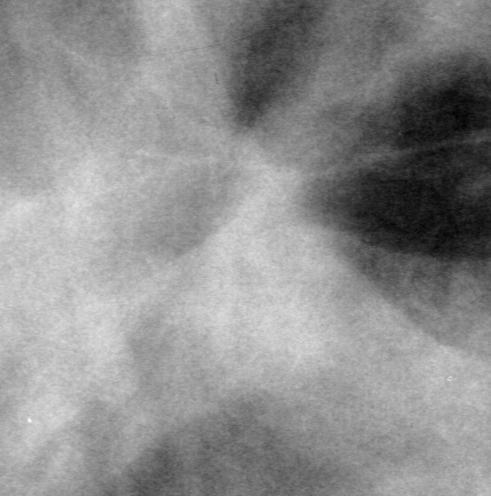
Region of interest cut from a scanned film mammogram (one marked finding), right breast, CC view, BI-RADS breast density category 4 (scale 1–4).
Finding: mass, shape architectural distortion; BI-RADS assessment category 5; pathology (as recorded): malignant.